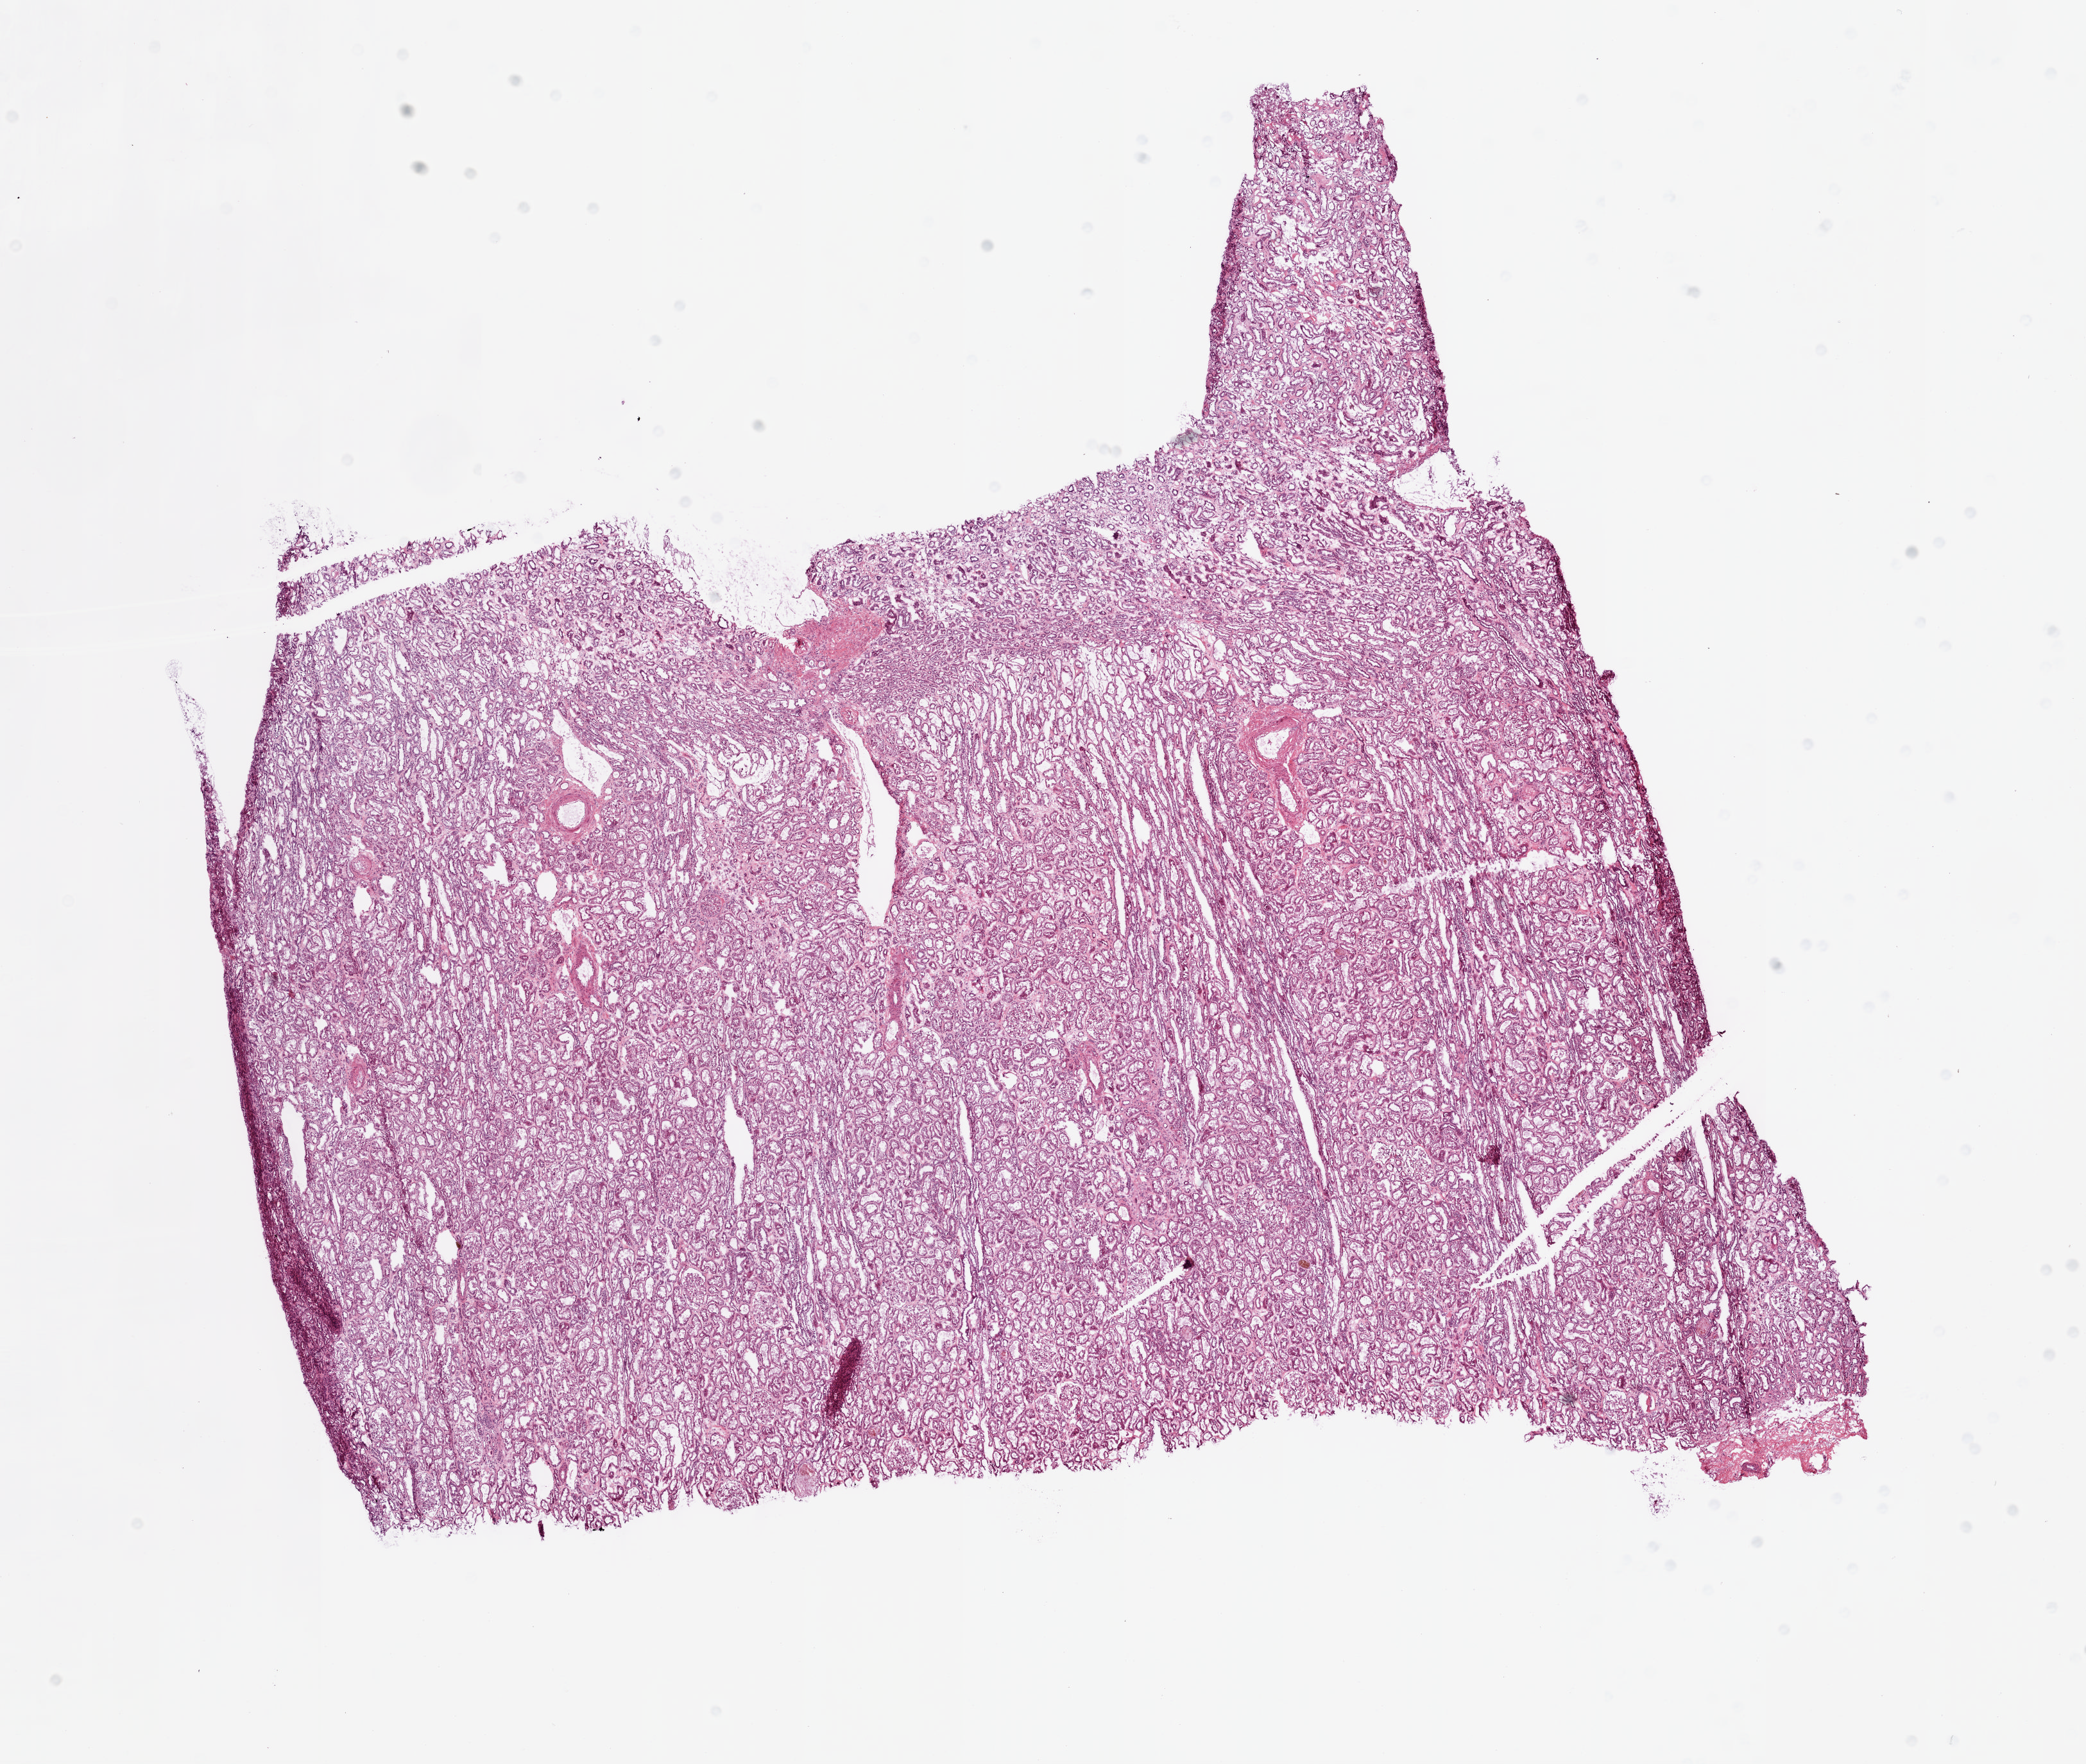
H&E whole-slide image — low-resolution overview of the scanned area, about 12.9 x 10.9 mm (acquisition: 20x scan), frozen section from the top of the tissue portion, sample: solid tissue normal (non-tumour tissue), kidney. Male patient; age at initial diagnosis 56 years.
This section: solid tissue normal (non-tumour) sample from the same patient. Patient diagnosis: Clear cell adenocarcinoma, NOS.